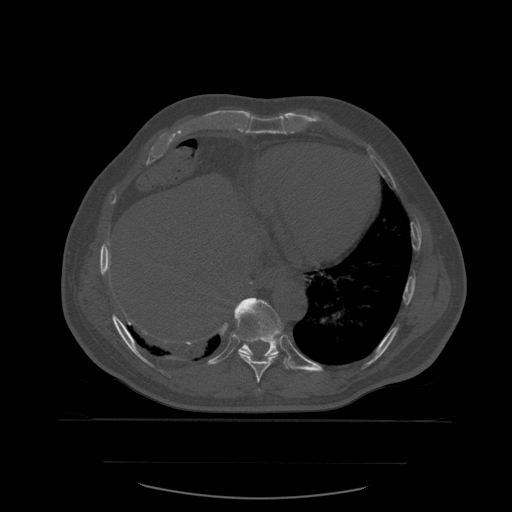
CT including the spine, one axial slice. Position 332 of 590 along the scan axis. Bone window (W 1800 / L 400 HU). 1.25 mm slice thickness. 512 × 512 image matrix, field of view 479 × 479 mm. Patient age 71 years. From the clinical record (not read from this slice): primary cancer: lung.
Outlined on this slice (semi-automatically segmented with operator editing):
- T10 vertebra: bounding box <234,298,289,370> (left, top, right, bottom; pixels)
- T9 vertebra: <238,335,279,383>